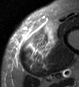
MRI of an extremity soft-tissue mass, one axial slice. STIR. MR volume resampled by the dataset authors to the PET/CT grid (not the native acquisition matrix). 3.27 mm slice thickness. 79 × 87 image matrix, field of view 77 × 85 mm. Male patient. Case-level facts recorded for this patient, not image findings: histological type: pleiomorphic leiomyosarcoma; grade: high; site of the primary tumour: left thigh.
Structures marked on this image (expert contour drawn on MRI and transferred to this co-registered scan by the dataset authors):
- gross tumour volume including surrounding oedema: bounding box [x1, y1, x2, y2] px = [20, 20, 57, 72]